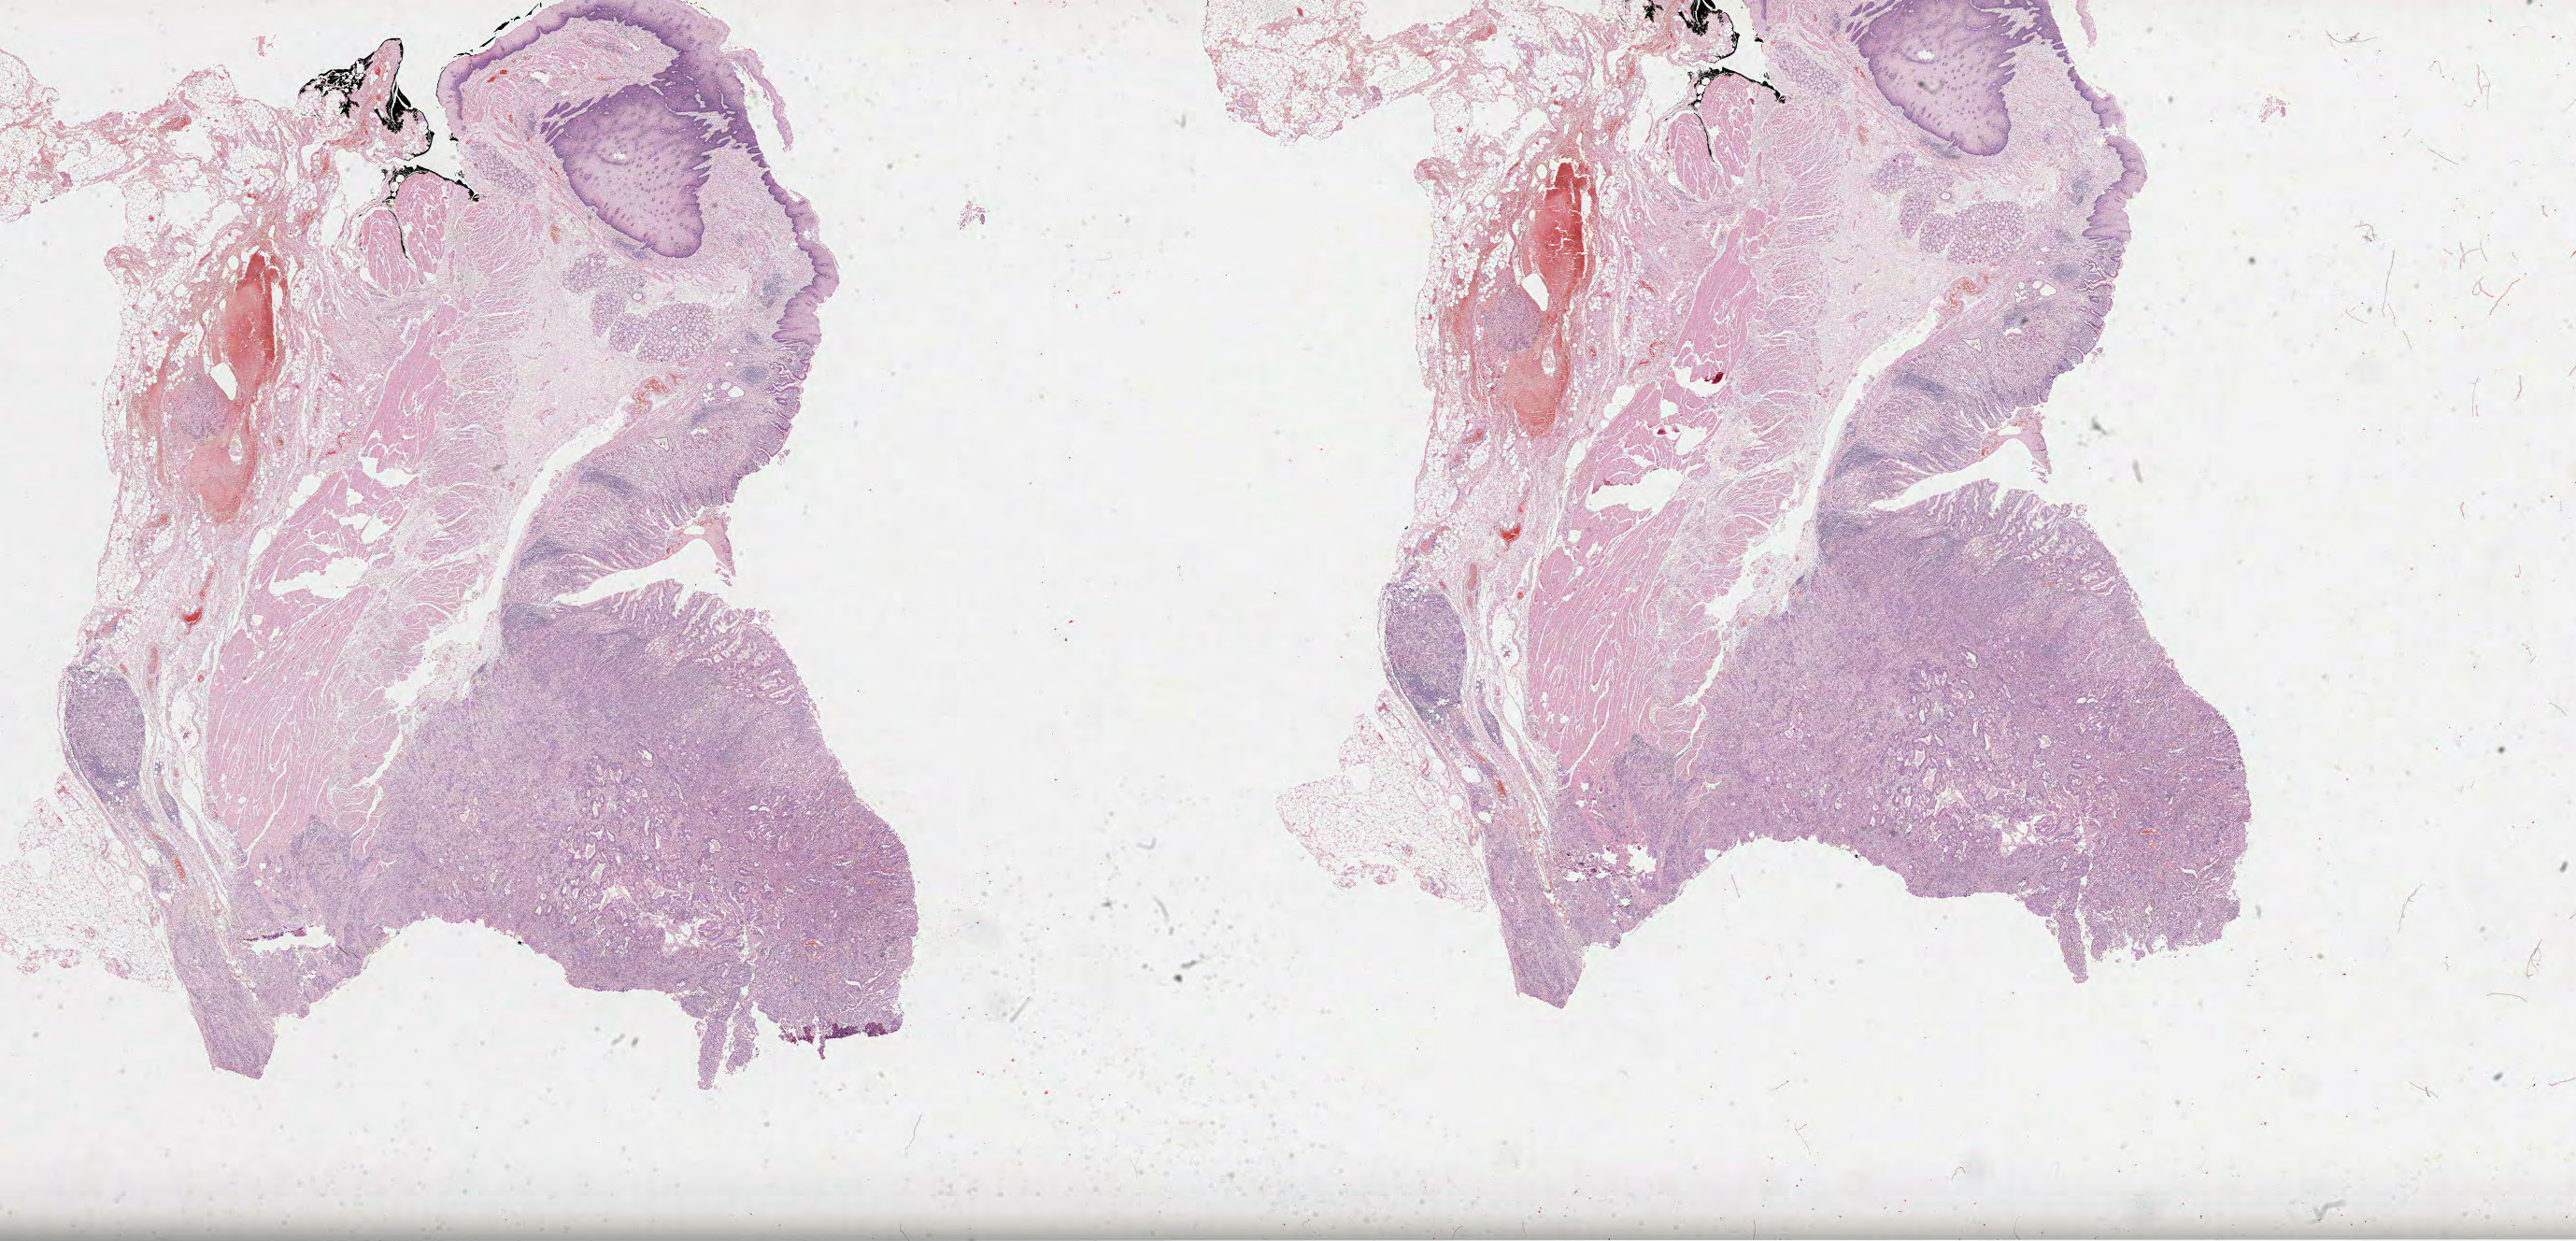
Whole-slide histology image, H&E, shown as a low-resolution overview of the whole scanned area (about 44.5 x 21.4 mm, acquisition: 40x scan); FFPE section; sample: primary tumour, stomach. Female, age 53 years at initial diagnosis. Histologic grade: G2 (moderately differentiated).
Diagnosis: Tubular adenocarcinoma (cardia, NOS). AJCC pathologic stage: IIIA (7th edition). Lymph nodes positive (case pathology): 19 of 34 examined. TNM: T2 N3 M0.